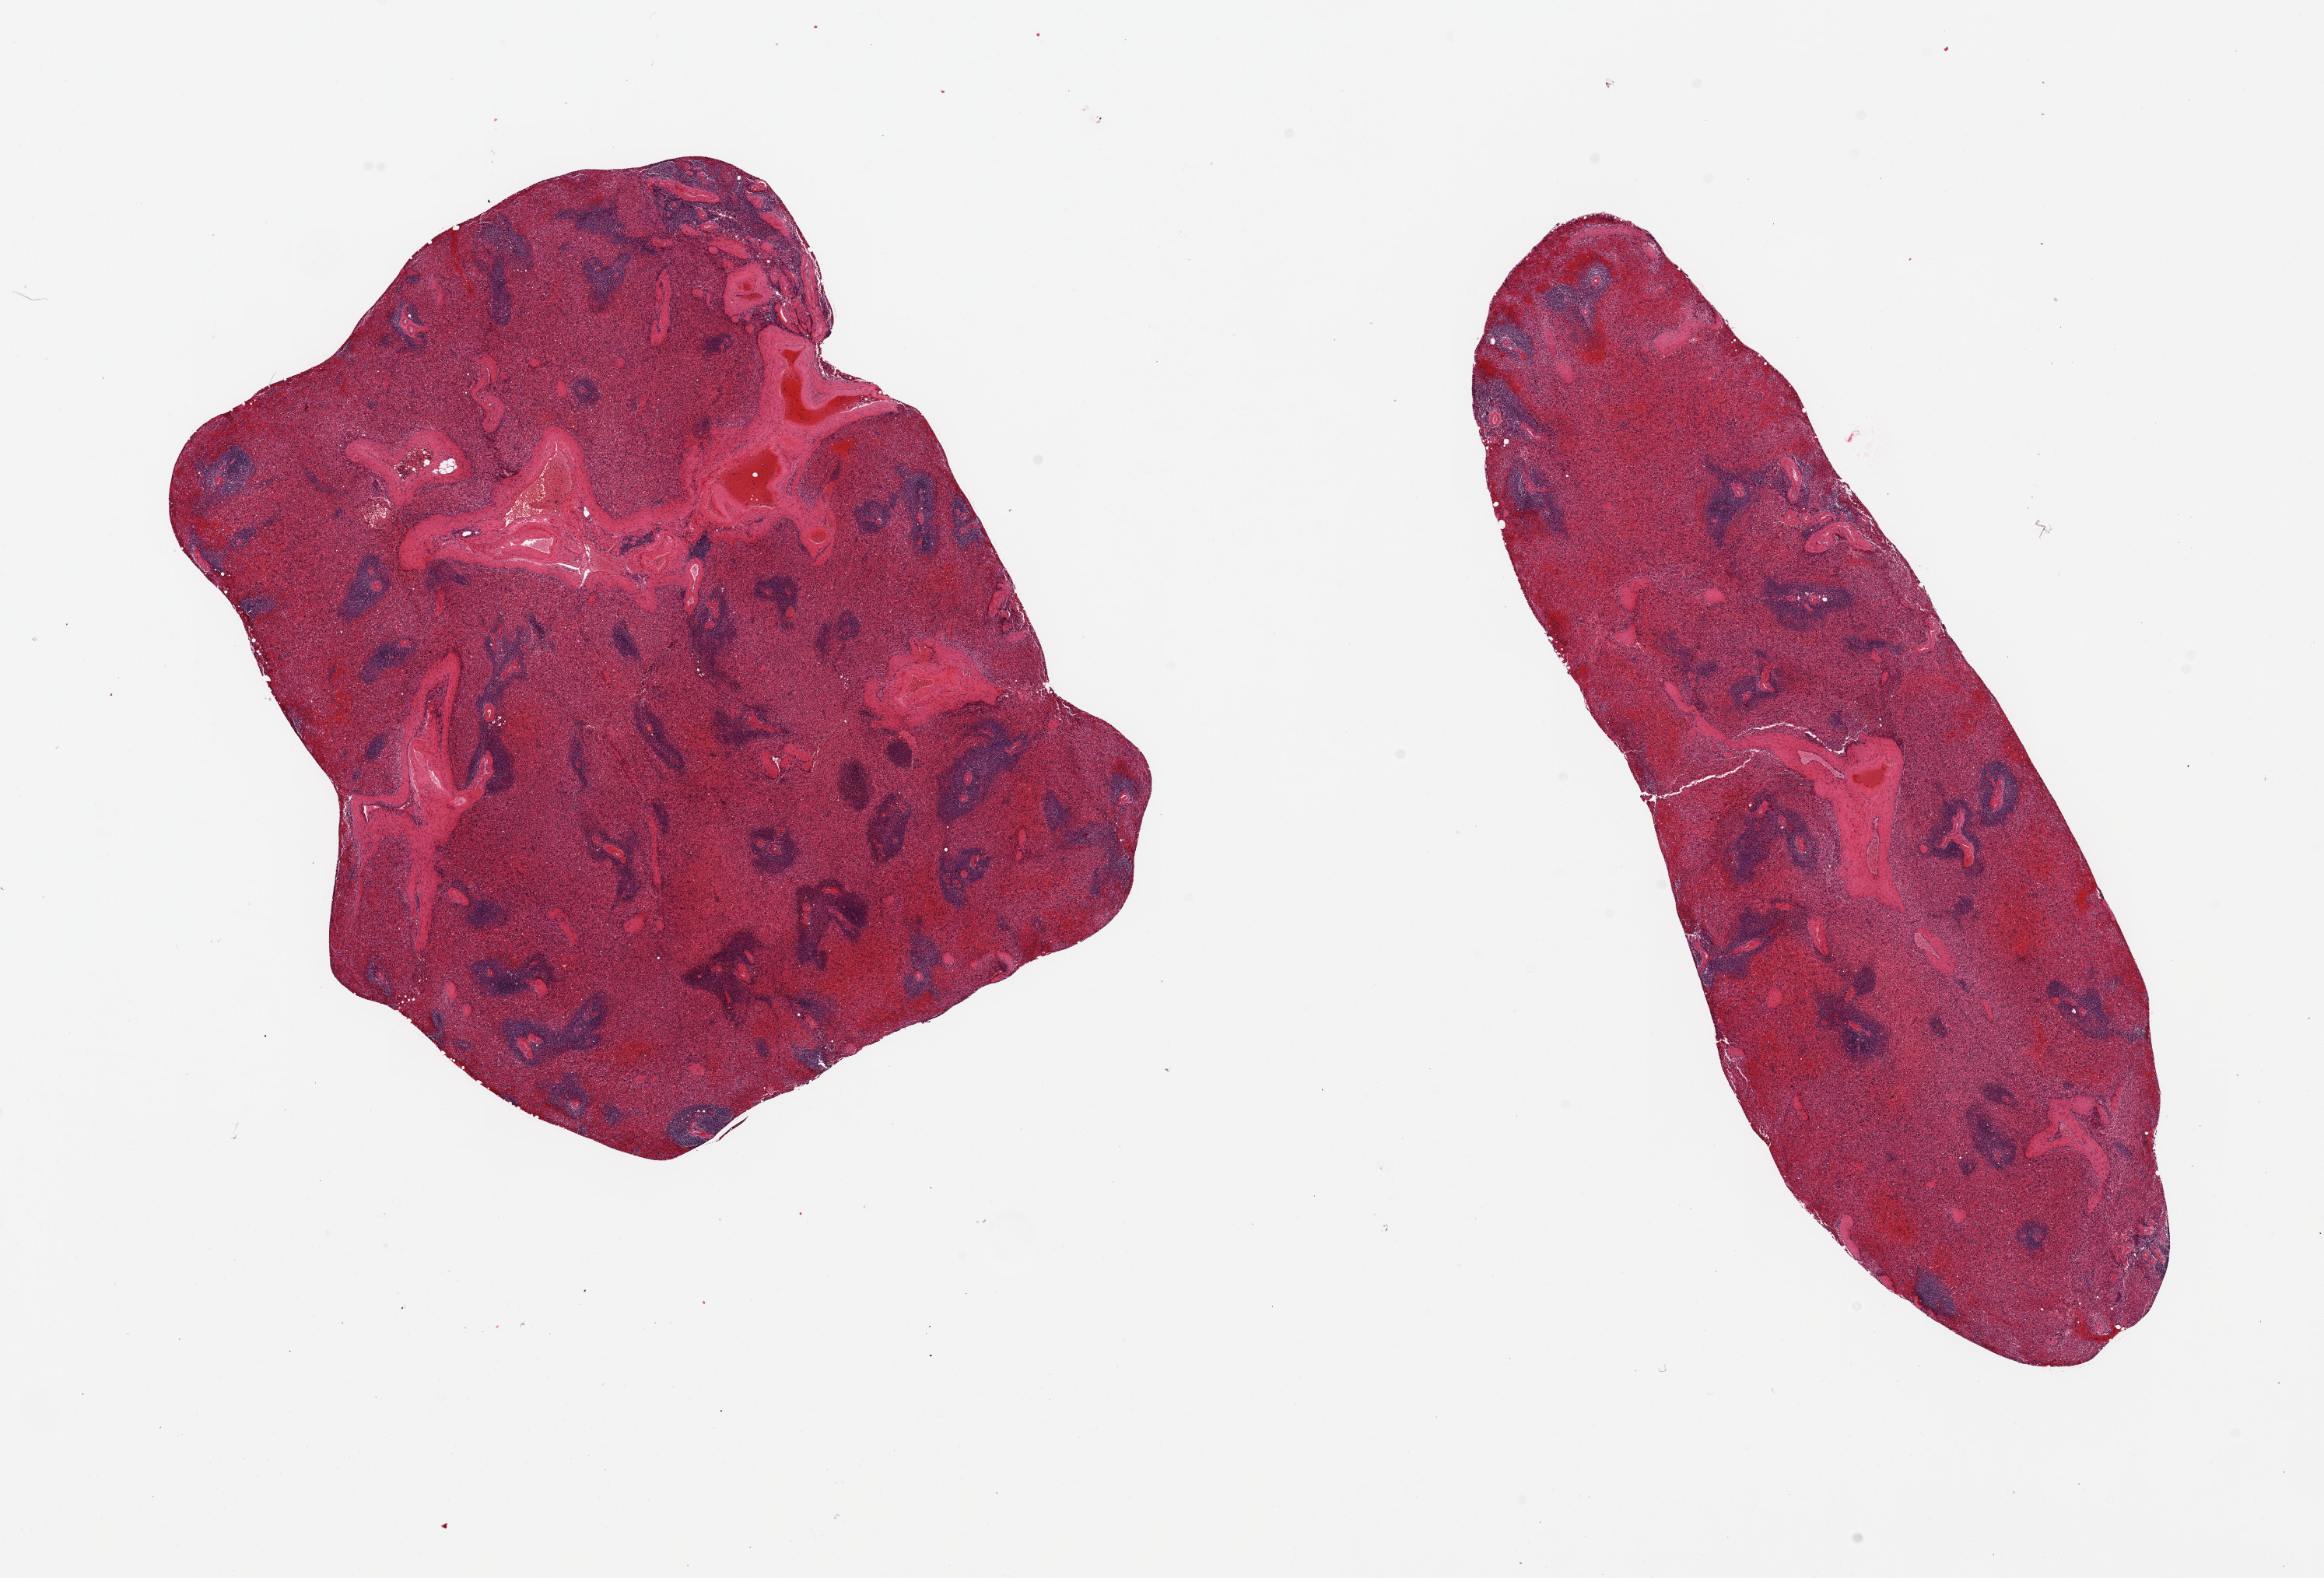
H&E whole-slide image — shown as a low-resolution overview of the whole scanned area (about 23.6 x 16.0 mm). PAXgene-fixed paraffin-embedded (PFPE) section. Sampled site (target tissue): spleen. Tissue donor sample. Donor sex: male.
Review note (as recorded): 2 pieces; congested.